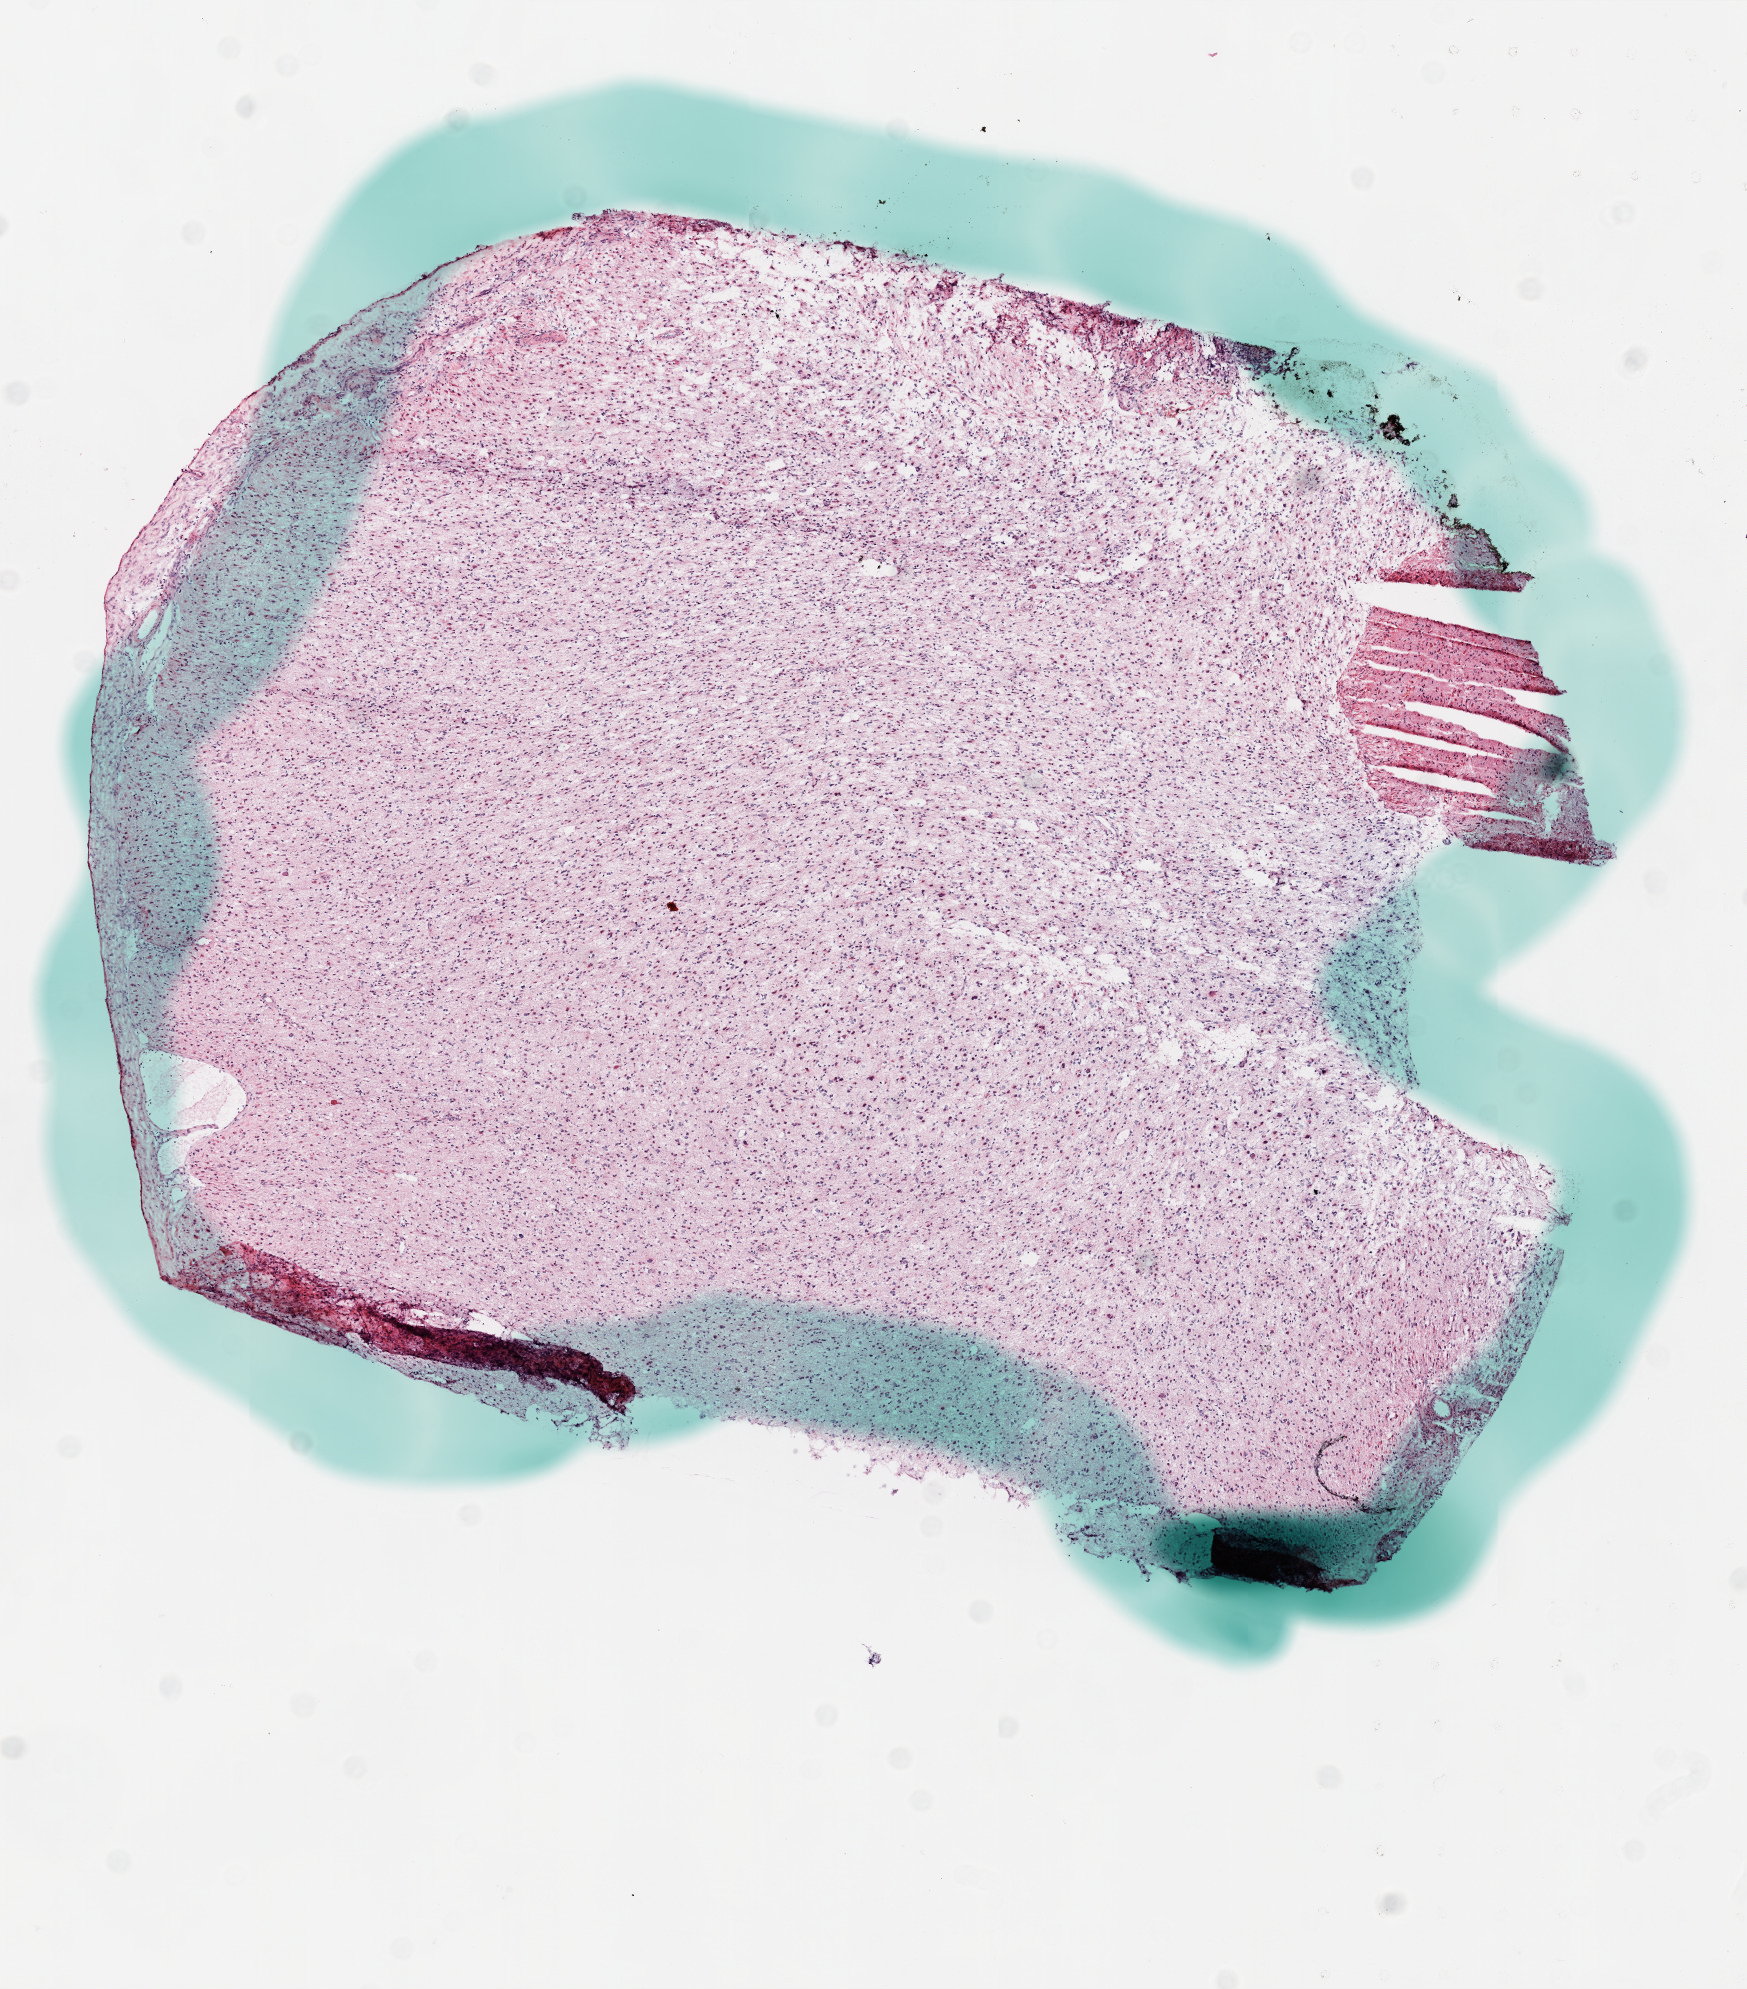
Hematoxylin and eosin (H&E) stained whole-slide image, shown as a low-resolution overview of the whole scanned area (about 7.0 x 8.0 mm, from a 20x scan), frozen section, primary tumour sample from the brain. Patient: male, age at initial diagnosis 64 years. Pathologist review of this section (percent, as recorded): tumour cells 90%, tumour nuclei 100%, normal cells 10%, stromal cells 0%, necrosis 0%.
Pathologic diagnosis: Glioblastoma.